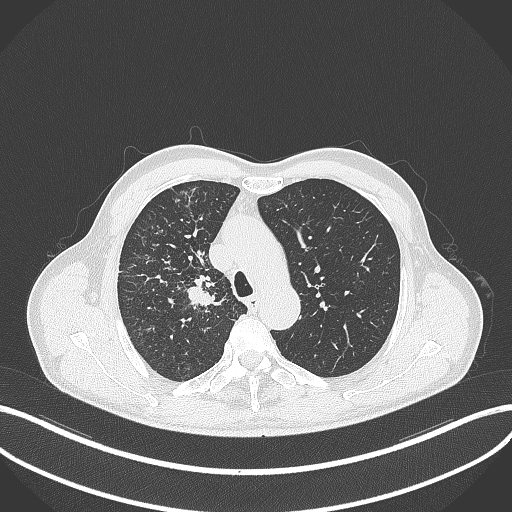
Chest CT, one axial slice; position 356 of 490 along the scan axis; reconstruction kernel B70f; lung window (W 1500 / L -600 HU); 1 mm slice thickness; 512 × 512 image matrix, field of view 400 × 400 mm. Male patient, age 69 years. From the clinical record (not read from this slice): clinical TNM (as recorded): T2a N0 M0.
Structures marked on this image (bounding box drawn by a radiologist):
- lung tumour (recorded histology: adenocarcinoma): bounding box [x1, y1, x2, y2] px = [184, 275, 227, 310]